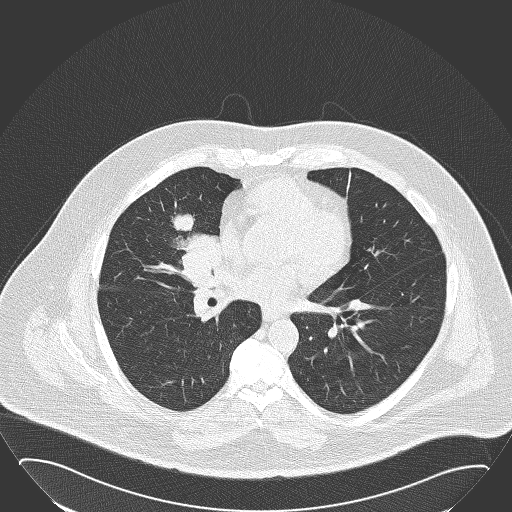
Low-dose screening chest CT, one axial slice. Position 79 of 168 along the scan axis. 120 kVp. Lung window (W 1500 / L -600 HU). 512 × 512 image matrix, field of view 432 × 432 mm.
Structures marked on this image (manually delineated by an expert):
- lesion 1 (tumor, hilum of right lung): bounding box (x1, y1, x2, y2) in pixels: (173, 214, 221, 278)